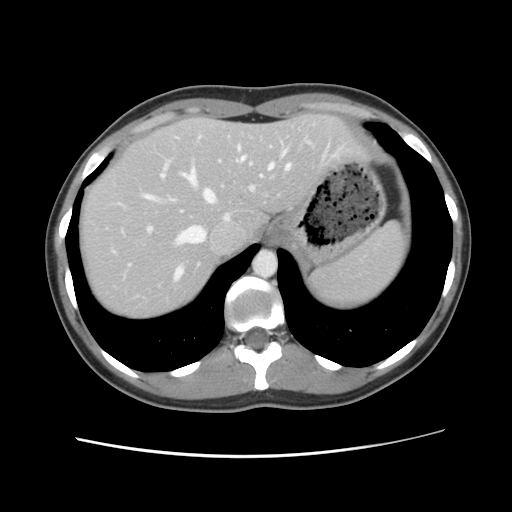
Contrast-enhanced abdominal CT, one axial slice; position 94 of 134 along the scan axis; intravenous contrast given; soft-tissue window (W 400 / L 40 HU); 2.5 mm slice thickness; 512 × 512 image matrix, field of view 339 × 339 mm. Female patient, age 33 years. Case-level facts recorded for this patient, not image findings: diagnosis: colorectal cancer liver metastases, imaged before liver resection; multiple liver metastases: yes; largest metastasis: 4.5 cm; disease in both lobes: yes.
Structures marked on this image (expert manual segmentation):
- hepatic veins: bounding box [x1, y1, x2, y2] px = [141, 136, 308, 280]
- liver: [79, 115, 365, 320]
- planned liver remnant (the part of the liver to remain after resection): [79, 115, 365, 320]
- portal vein (with intrahepatic branches): [112, 201, 154, 234]